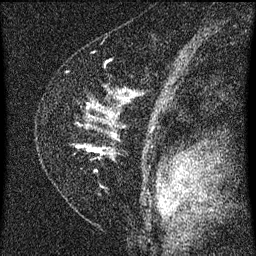
Breast MRI (dynamic contrast-enhanced), one sagittal slice. Slice 44 of 60 in the series (ordered by position). Dynamic contrast-enhanced series, image 2 of 3 at this slice position (ordered by acquisition). 1.5 T. TE 4.2 ms, TR 8 ms. 2 mm slice thickness. 256 × 256 image matrix, field of view 180 × 180 mm. Patient: female, 47 years.
Structures marked on this image (semi-automatic segmentation, software-assisted and operator-edited):
- analysis volume of interest (the breast-tissue region the enhancement analysis was run in; not a lesion): bounding box [x1, y1, x2, y2] px = [75, 90, 134, 189]
- tumour enhancement mask (voxels above the 70 % enhancement threshold inside the analysis volume of interest): [80, 146, 102, 151]